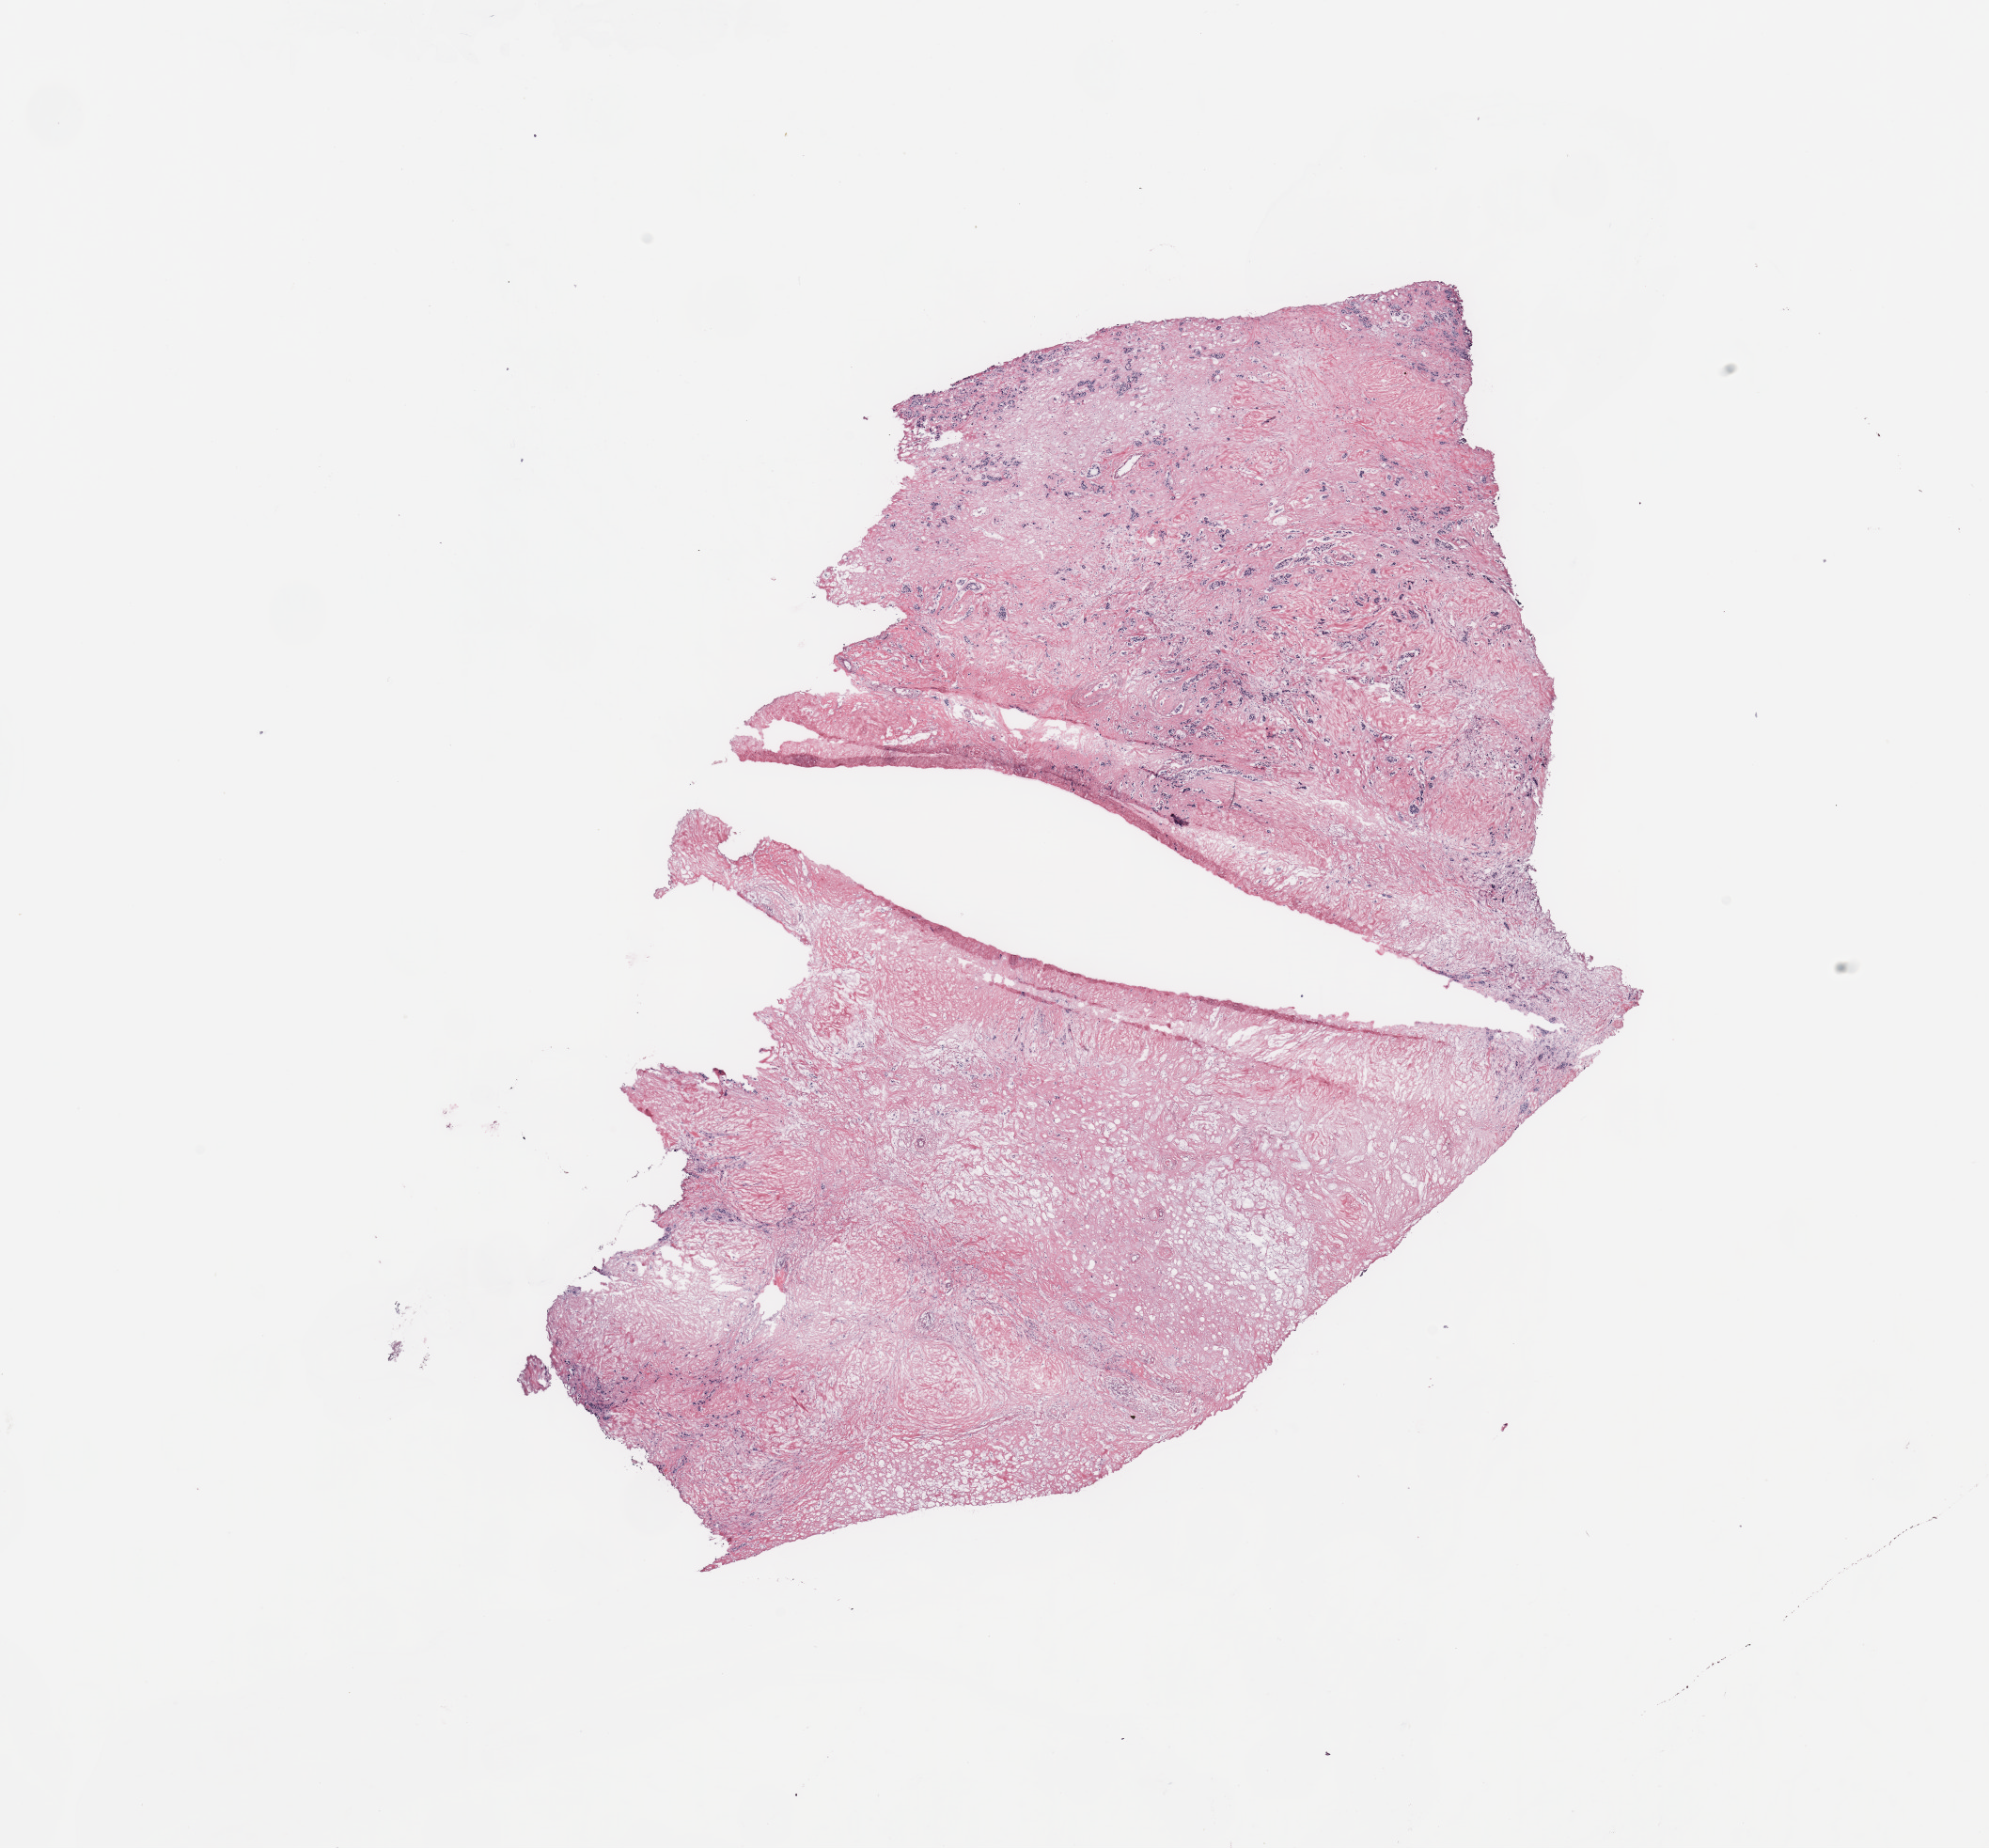
Digitized H&E tissue section (whole slide), whole scanned area (about 16.7 x 15.5 mm) shown as a low-resolution overview; breast, tissue type not recorded.
* patient diagnosis (cohort enrolment): breast cancer (breast)